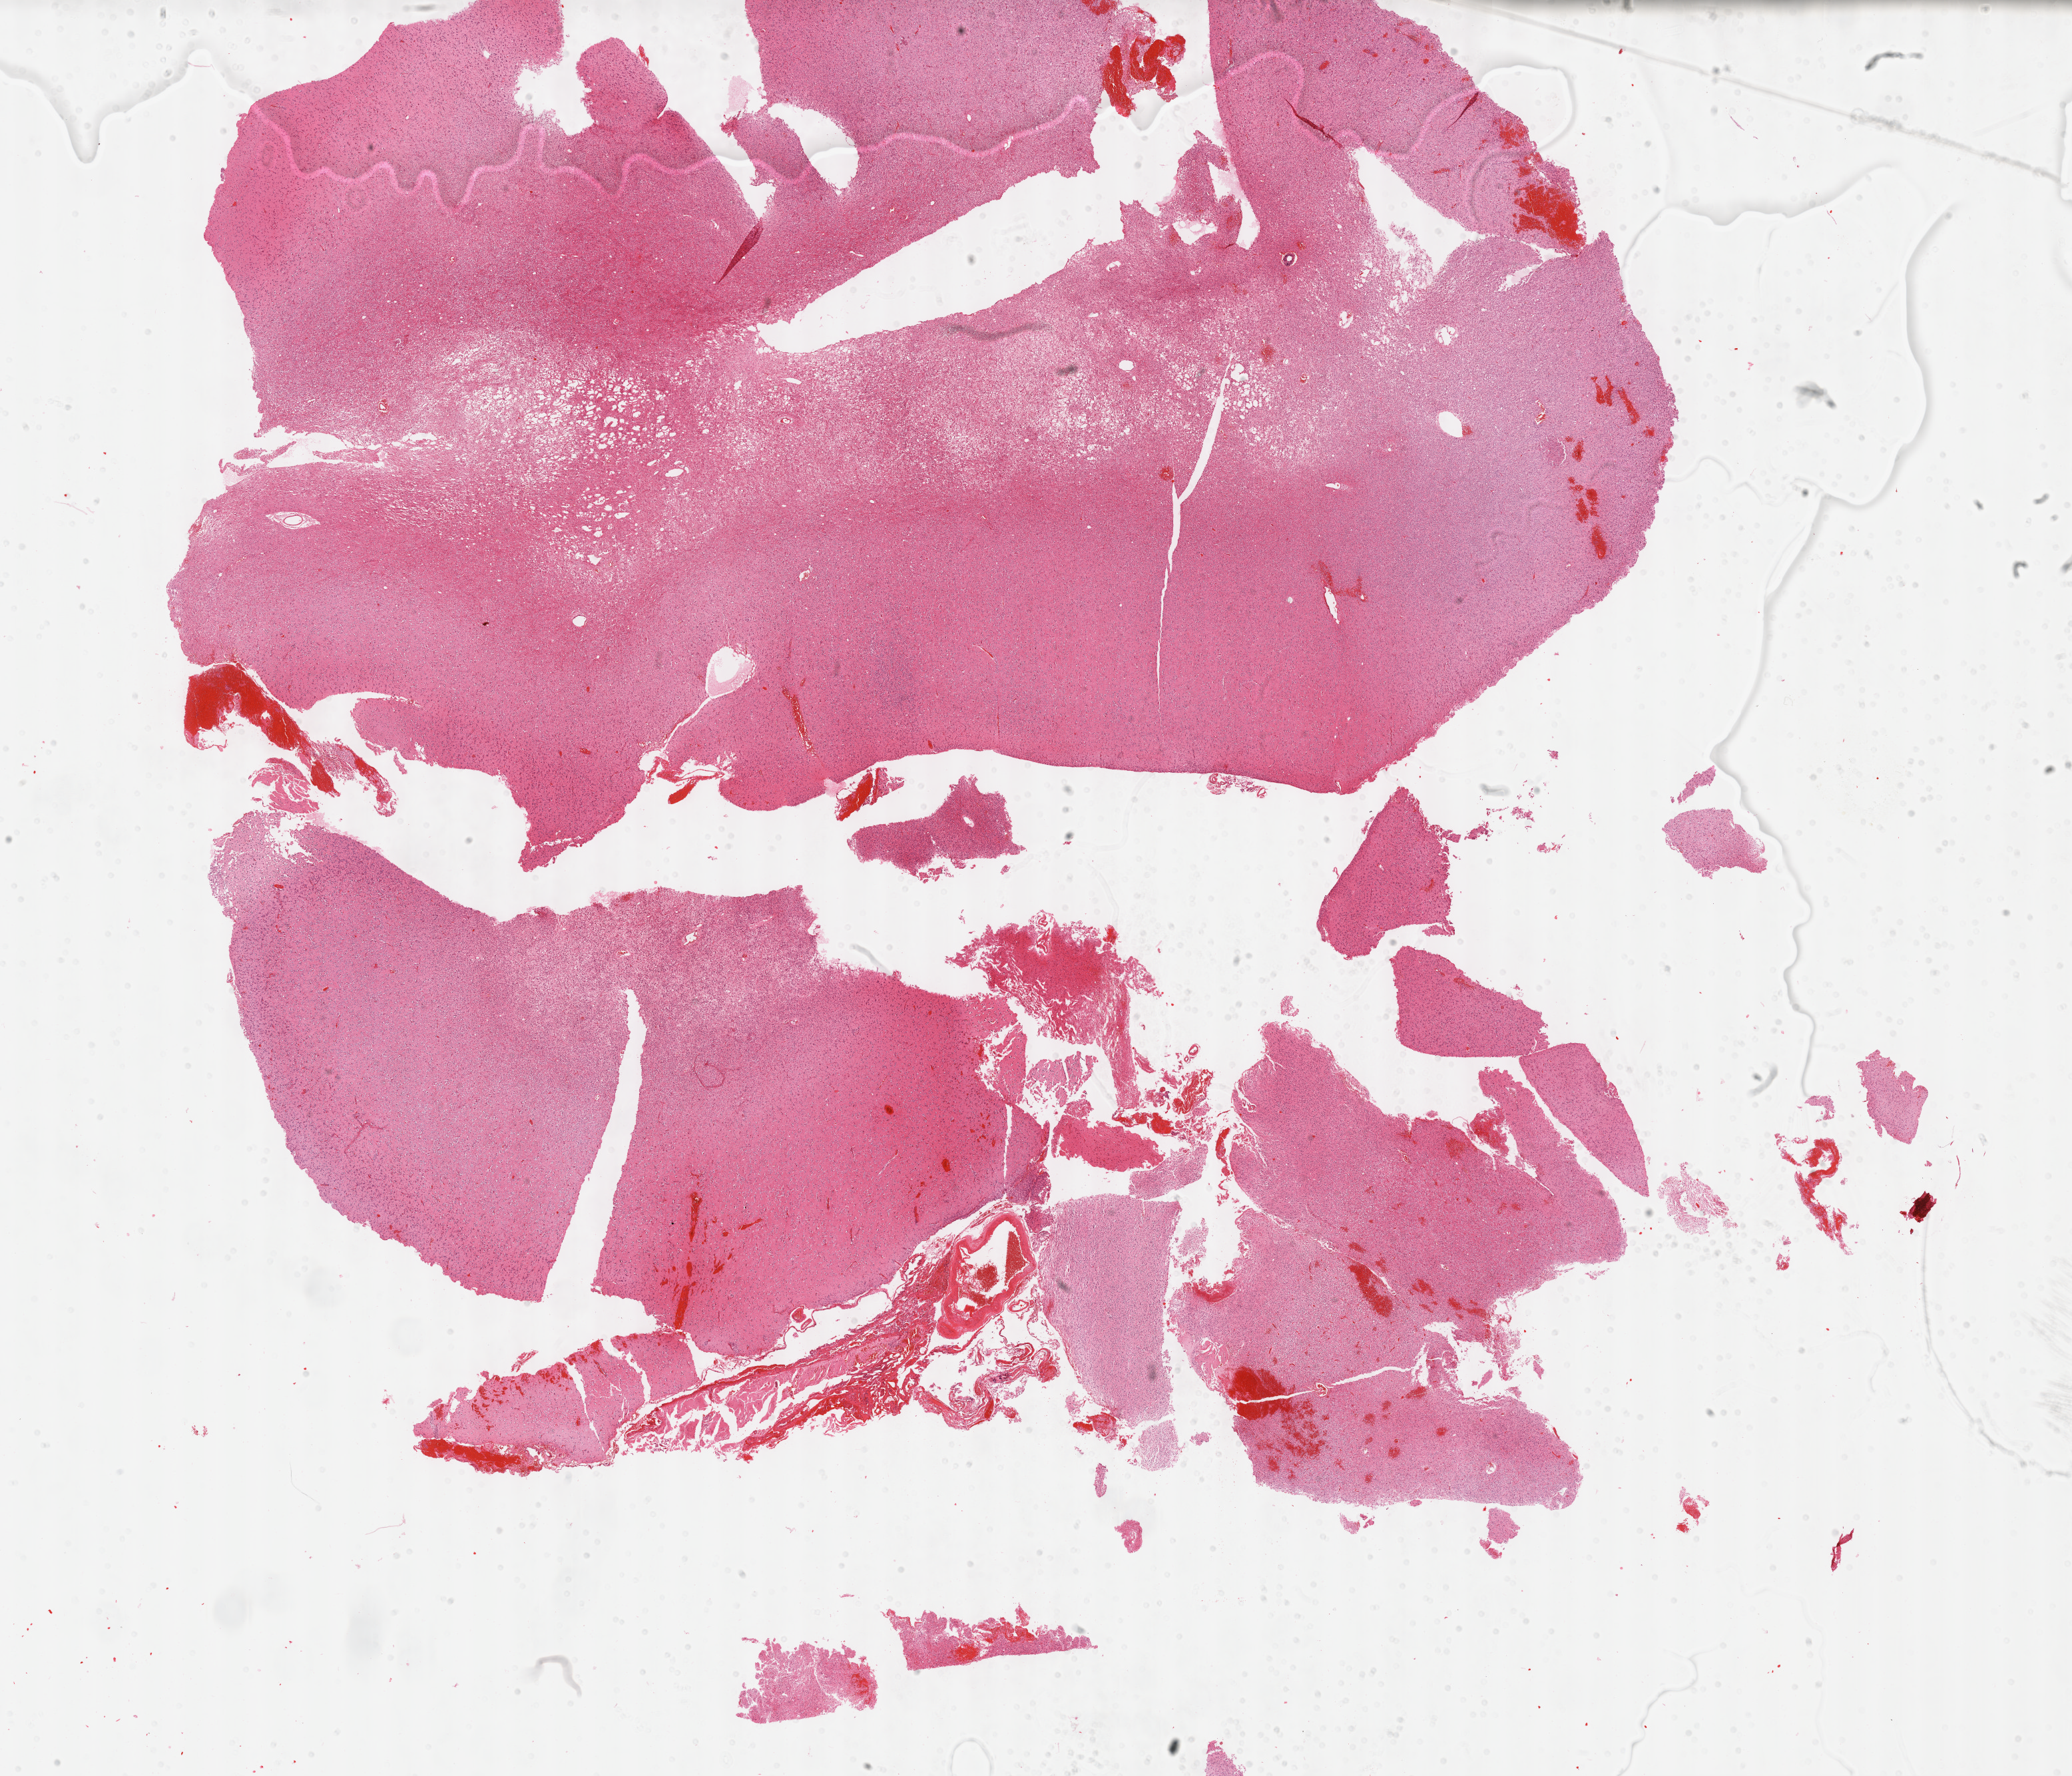
Whole-slide histology image, H&E-stained, a low-resolution overview of the entire scanned area, about 25.2 x 21.6 mm, formalin-fixed paraffin-embedded (FFPE) diagnostic section, primary tumour sample from the brain. Male patient; age at initial diagnosis 43 years. Histologic grade: G2 (moderately differentiated).
Pathologic diagnosis: Oligodendroglioma, NOS. Laterality: right.